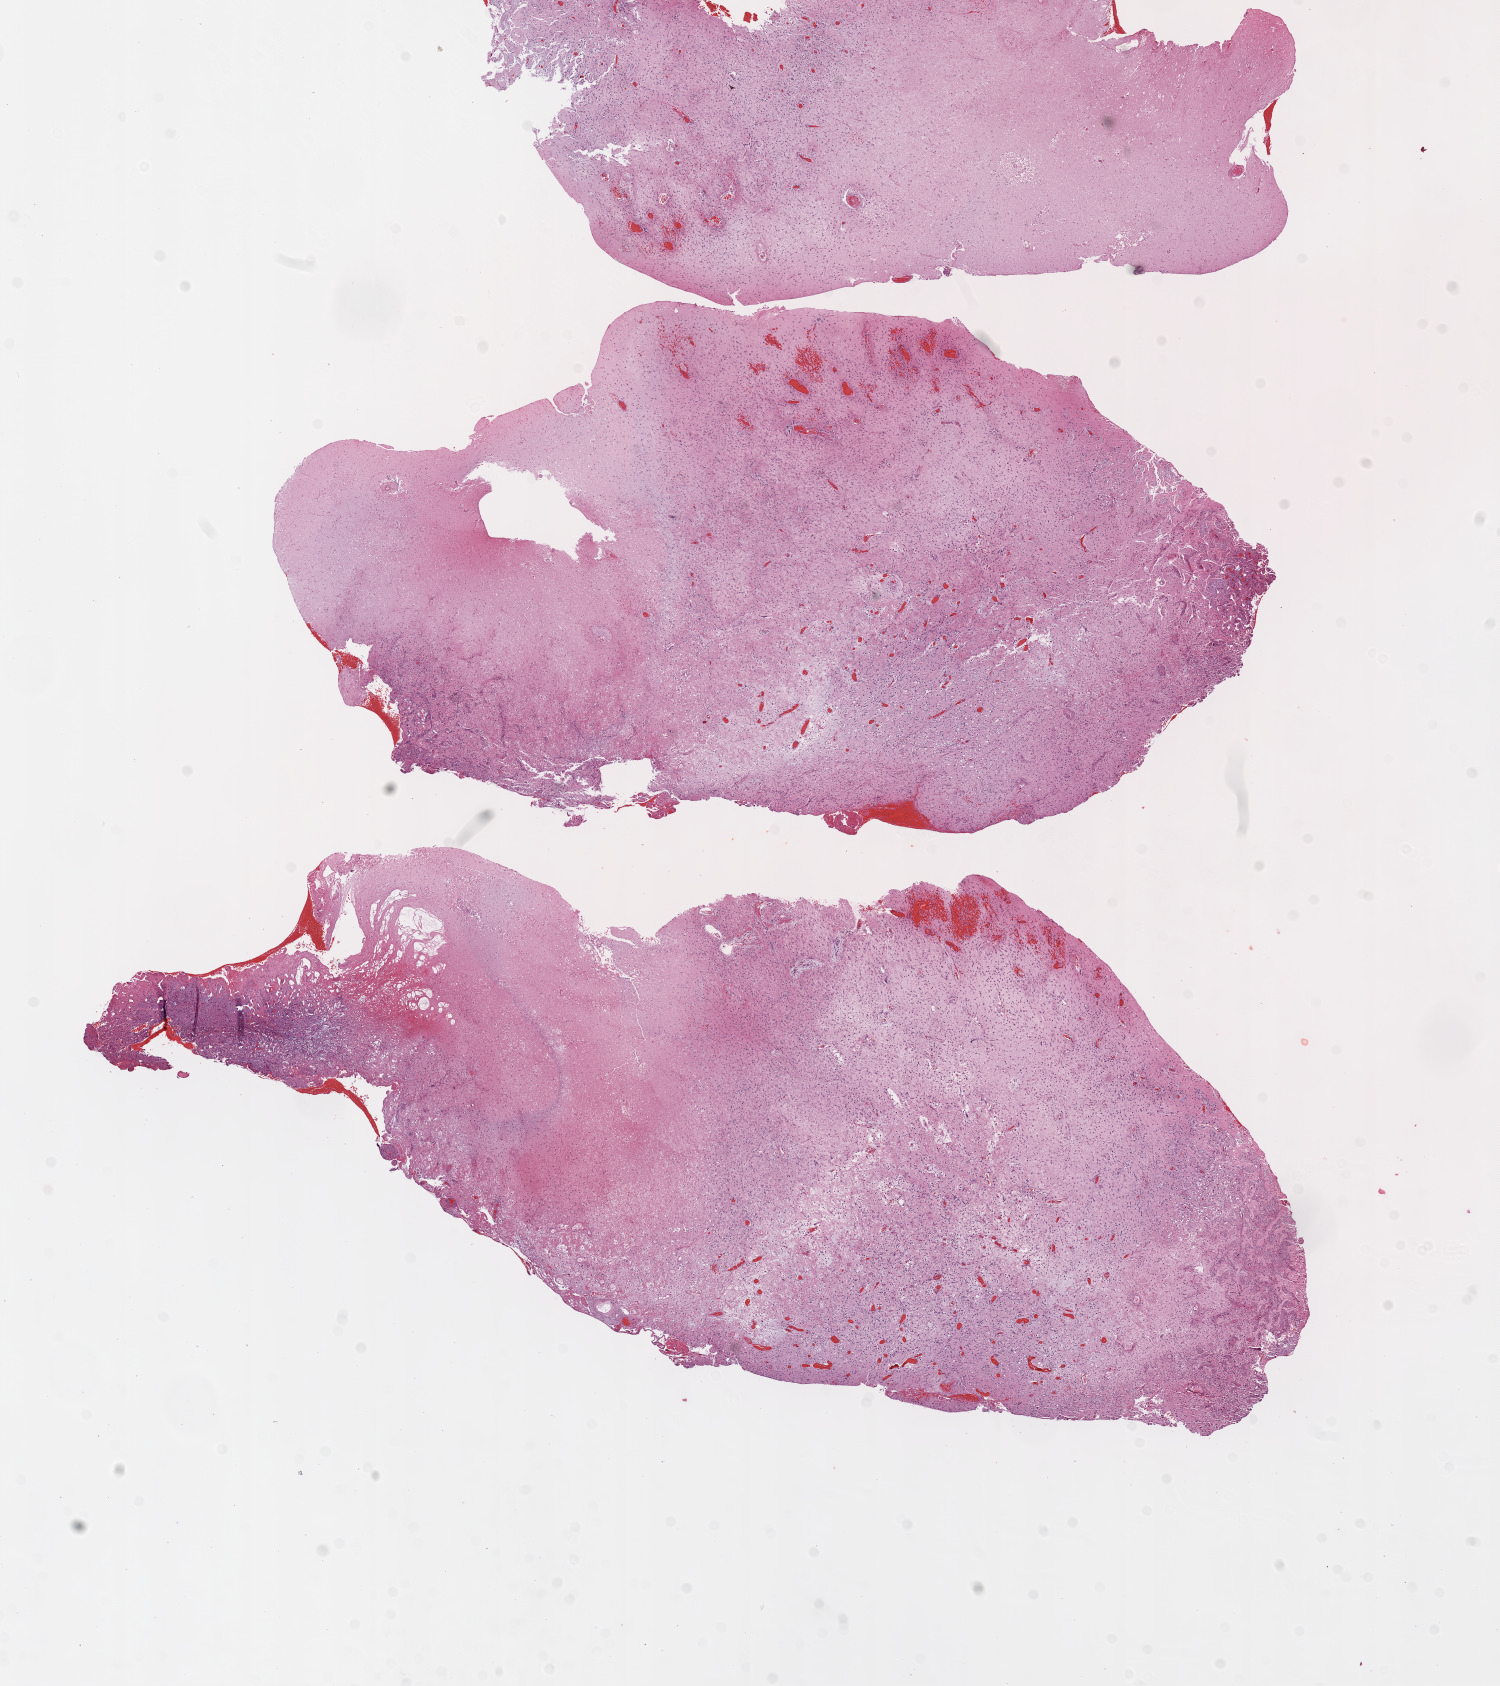
Digitized Hematoxylin and eosin (H&E) stained tissue section (whole slide) — whole scanned area (about 12.0 x 13.5 mm, acquisition: 20x scan) shown as a low-resolution overview; formalin-fixed paraffin-embedded (FFPE) diagnostic section; brain, primary tumour sample. Patient: female, age at initial diagnosis 75 years.
• pathologic diagnosis: Glioblastoma